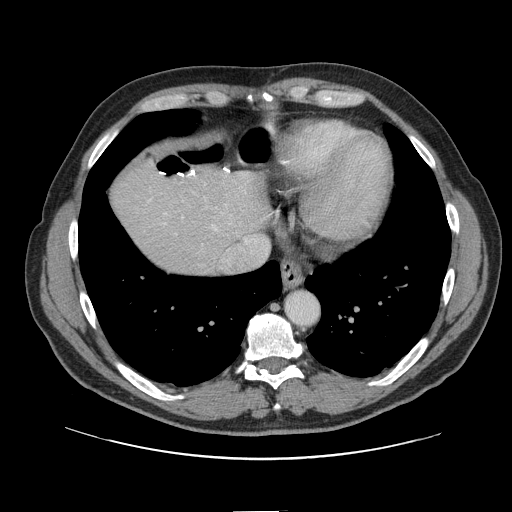
Contrast-enhanced abdominal CT, one axial slice; position 132 of 161 along the scan axis; 120 kVp; intravenous contrast given; soft-tissue window (W 400 / L 40 HU); 512 × 512 image matrix, field of view 412 × 412 mm. Male patient, age 66 years. From the clinical record (not read from this slice): diagnosis: colorectal cancer liver metastases, imaged before liver resection; multiple liver metastases: no; largest metastasis: 3.5 cm; chemotherapy before resection: yes.
Structures marked on this image (outlined manually by an expert reader):
- hepatic veins: box from (x=149, y=184) to (x=232, y=264) px
- liver: (x=112, y=163)–(x=267, y=275)
- planned liver remnant (the part of the liver to remain after resection): (x=112, y=164)–(x=267, y=273)